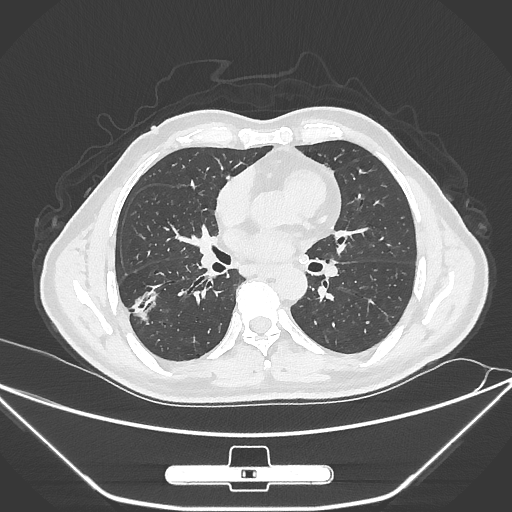
Chest CT, one axial slice. Position 146 of 310 along the scan axis. Reconstruction kernel IMR1,SharpPlus. Lung window (W 1500 / L -600 HU). 1 mm slice thickness. 512 × 512 image matrix. Patient: male, 71 years. From the clinical record (not read from this slice): clinical TNM (as recorded): T1c N0 M0.
Structures marked on this image (bounding box drawn by a radiologist):
- lung tumour (recorded histology: adenocarcinoma): box from (x=127, y=286) to (x=169, y=333) px